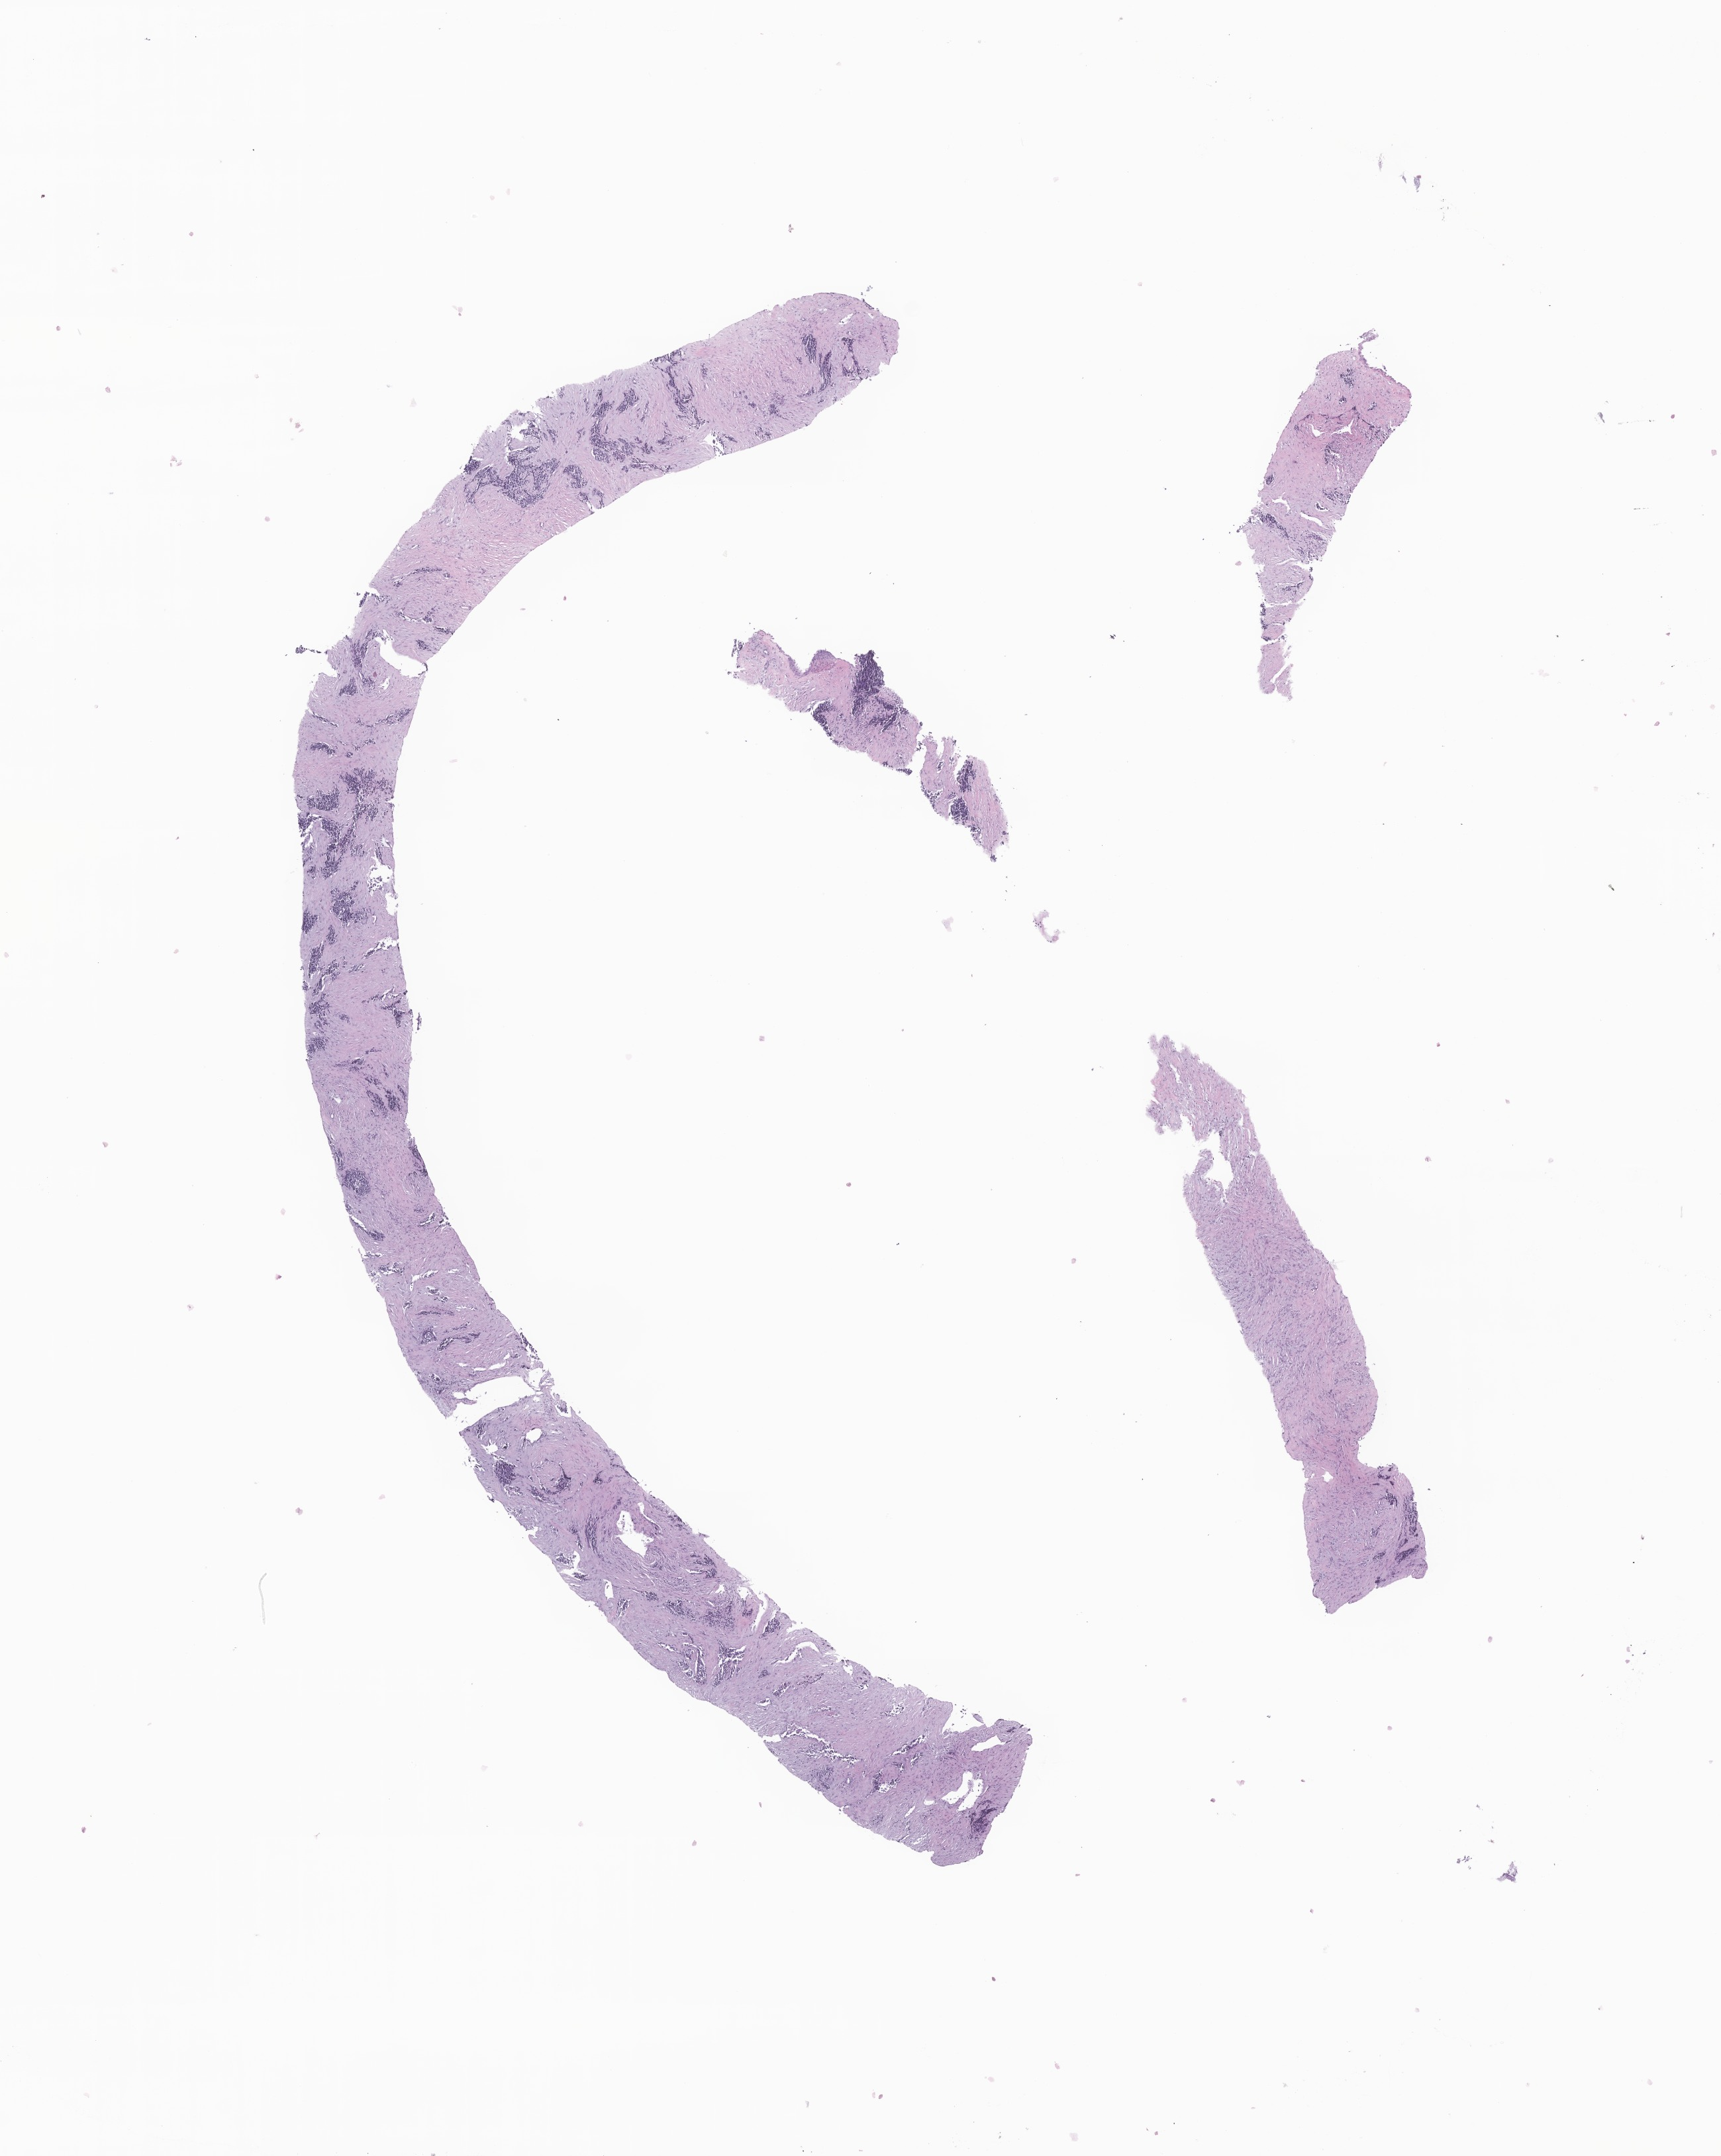
Whole-slide image, H&E stain of tumor tissue from the abdomen — a low-resolution overview of the entire scanned area, about 11.0 x 13.7 mm. FFPE section. Male patient, age 231 months.
Diagnosis (ICD-O-3 morphology term): Desmoplastic small round cell tumor.